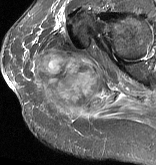
MRI of an extremity soft-tissue mass, one axial slice; position 38 of 57 along the scan axis; STIR; MR volume resampled by the dataset authors to the PET/CT grid (not the native acquisition matrix); 3.27 mm slice thickness; 156 × 165 image matrix, field of view 152 × 161 mm. Female patient. Case-level facts recorded for this patient, not image findings: histological type: epithelioid sarcoma with vascular differentiation; site of the primary tumour: right buttock.
Structures marked on this image (expert contour drawn on MRI and transferred to this co-registered scan by the dataset authors):
- gross tumour volume (mass): bounding box (x1, y1, x2, y2) in pixels: (33, 51, 107, 113)